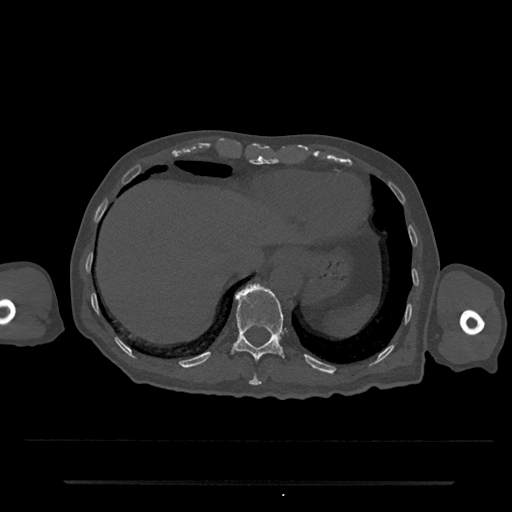
CT including the spine, one axial slice. Position 257 of 797 along the scan axis. 120 kVp. Bone window (W 1800 / L 400 HU). 0.5 mm slice thickness. 512 × 512 image matrix. Patient: male, 74 years. Case-level facts recorded for this patient, not image findings: primary cancer: prostate.
Outlined on this slice (semi-automatically segmented with operator editing):
- T10 vertebra: bounding box (x1, y1, x2, y2) in pixels: (249, 374, 261, 386)
- T11 vertebra: (231, 283, 287, 362)